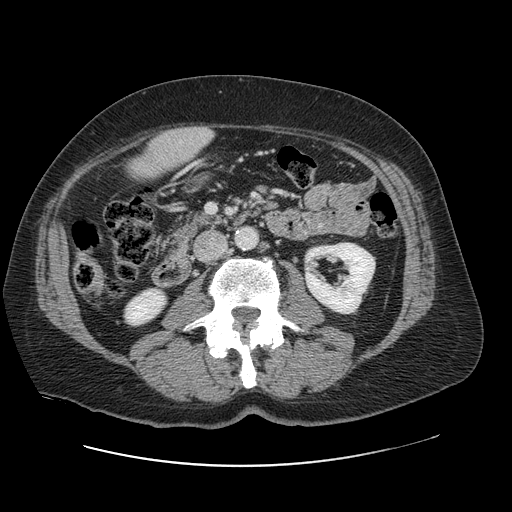
Contrast-enhanced abdominal CT, one axial slice; position 17 of 138 along the scan axis; 120 kVp; intravenous contrast given; soft-tissue window (W 400 / L 40 HU); 2.5 mm slice thickness; 512 × 512 image matrix, field of view 402 × 402 mm. Male patient, age 71 years. Case-level facts recorded for this patient, not image findings: diagnosis: colorectal cancer liver metastases, imaged before liver resection; multiple liver metastases: no; largest metastasis: 3.3 cm; disease in both lobes: no.
Annotated regions visible in this slice (expert manual segmentation):
- liver: box from (x=129, y=128) to (x=212, y=180) px
- planned liver remnant (the part of the liver to remain after resection): (x=130, y=141)–(x=170, y=180)